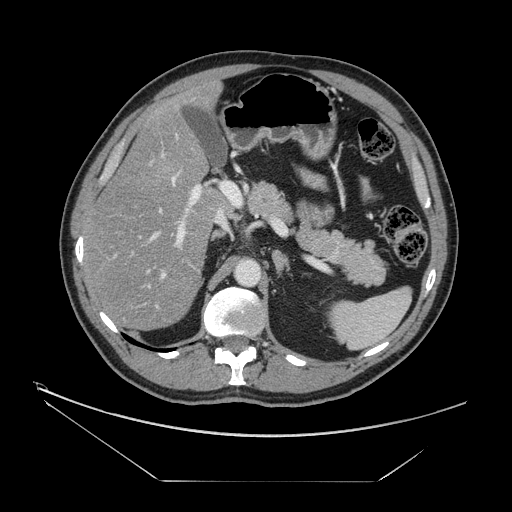
Contrast-enhanced abdominal CT, one axial slice. Slice 86 of 161 in the series (ordered by position). Reconstruction kernel STANDARD. 120 kVp. Intravenous contrast given. Soft-tissue window (W 400 / L 40 HU). 2.5 mm slice thickness. 512 × 512 image matrix. Male patient, age 65 years. From the clinical record (not read from this slice): diagnosis: colorectal cancer liver metastases, imaged before liver resection; multiple liver metastases: yes; largest metastasis: 4.2 cm; disease in both lobes: yes.
Structures marked on this image (expert manual segmentation):
- hepatic veins: bounding box (x1, y1, x2, y2) in pixels: (139, 170, 181, 288)
- liver: (85, 86, 226, 329)
- planned liver remnant (the part of the liver to remain after resection): (90, 86, 224, 330)
- portal vein (with intrahepatic branches): (112, 154, 221, 320)